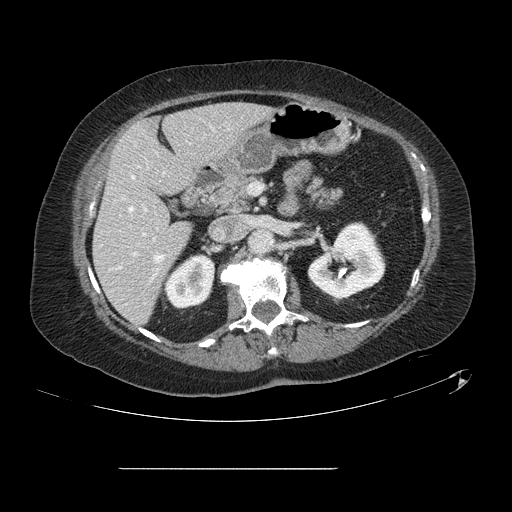
Contrast-enhanced abdominal CT, one axial slice; slice 60 of 148 in the series (ordered by position); 120 kVp; intravenous contrast given; soft-tissue window (W 400 / L 40 HU); 2.5 mm slice thickness; 512 × 512 image matrix. Female patient, age 75 years. From the clinical record (not read from this slice): diagnosis: colorectal cancer liver metastases, imaged before liver resection; multiple liver metastases: no; largest metastasis: 2.4 cm; chemotherapy before resection: no.
Outlined on this slice (outlined manually by an expert reader):
- hepatic veins: box from (x=129, y=176) to (x=163, y=262) px
- liver: (x=94, y=103)–(x=270, y=324)
- planned liver remnant (the part of the liver to remain after resection): (x=94, y=103)–(x=271, y=324)
- portal vein (with intrahepatic branches): (x=134, y=208)–(x=146, y=255)